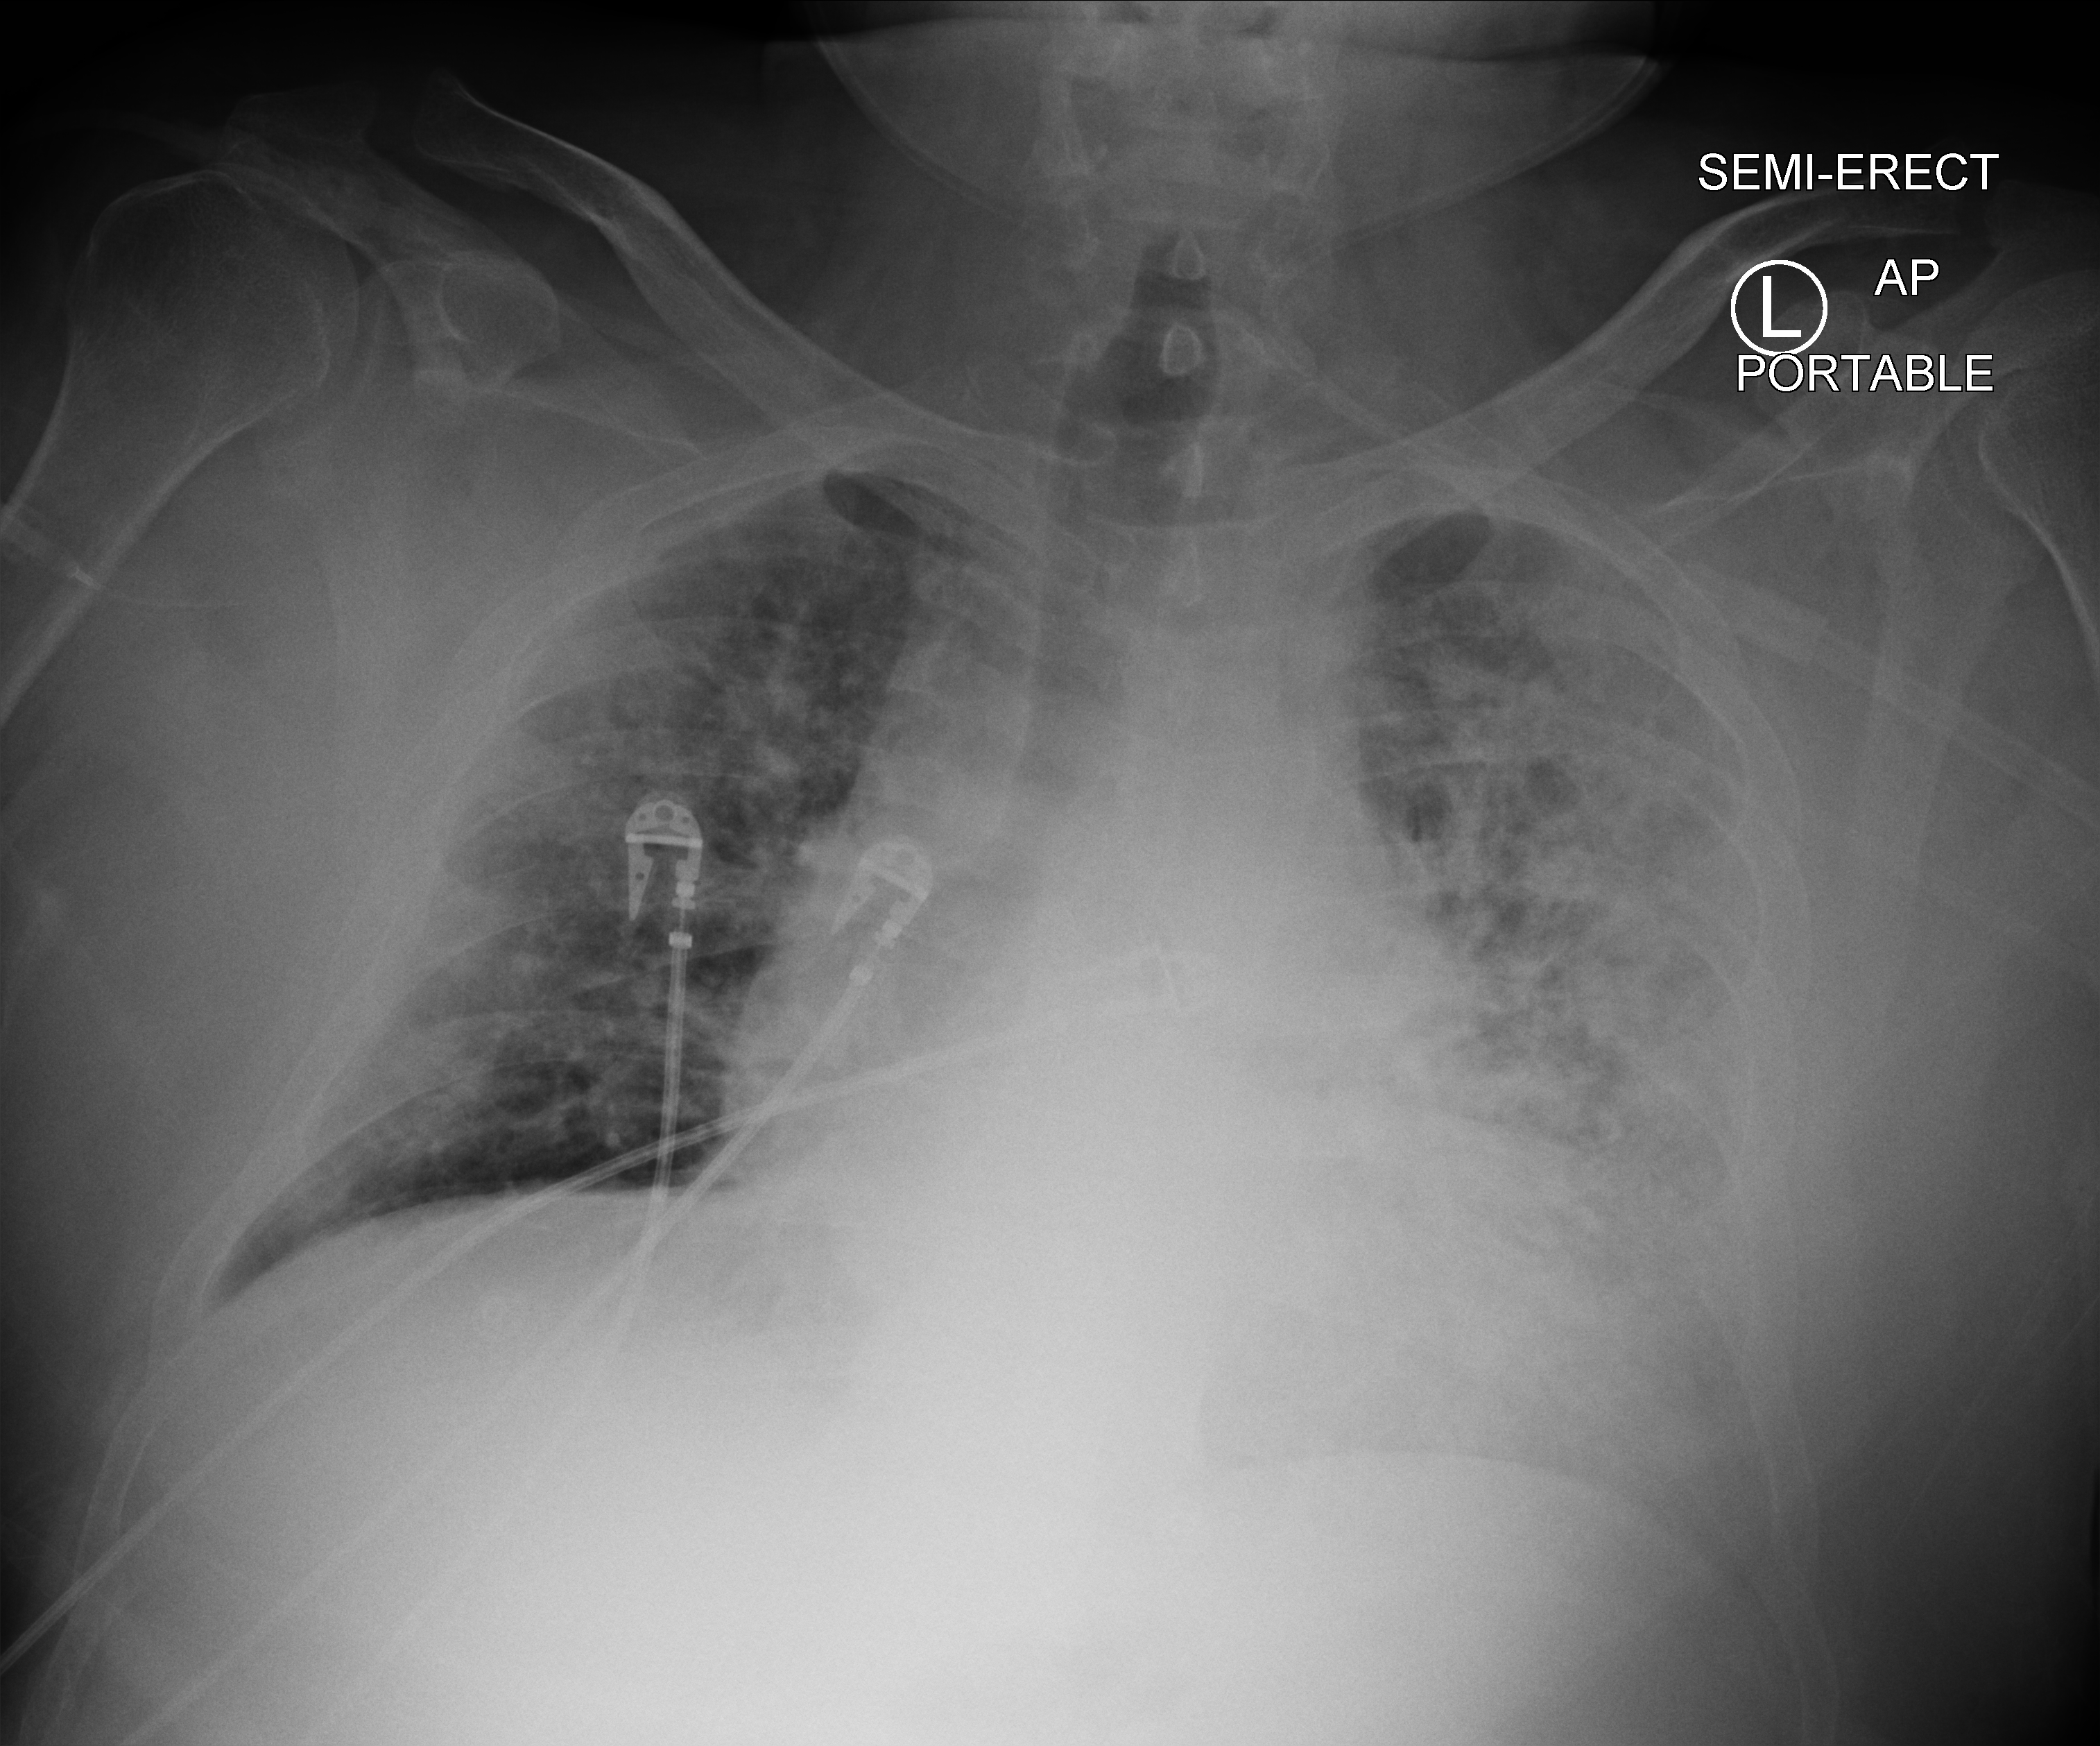
Chest X-ray (portable), anteroposterior (AP) projection. Male patient hospitalised with COVID-19, age 18–59 years.
From the hospital-stay record, not from the radiograph (when in the stay this image was taken is not recorded):
- diabetes (admission record): no
- hypertension (admission record): yes
- admitted to intensive care during this hospital stay: no